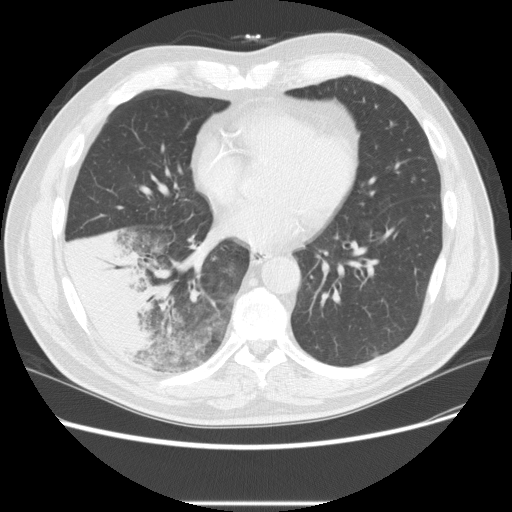
Low-dose screening chest CT, one axial slice; position 94 of 233 along the scan axis; lung window (W 1500 / L -600 HU); 512 × 512 image matrix, field of view 380 × 380 mm.
Outlined on this slice (expert manual segmentation):
- lesion 3 (tumor, lower lobe of right lung): bounding box [x1, y1, x2, y2] px = [68, 228, 169, 355]